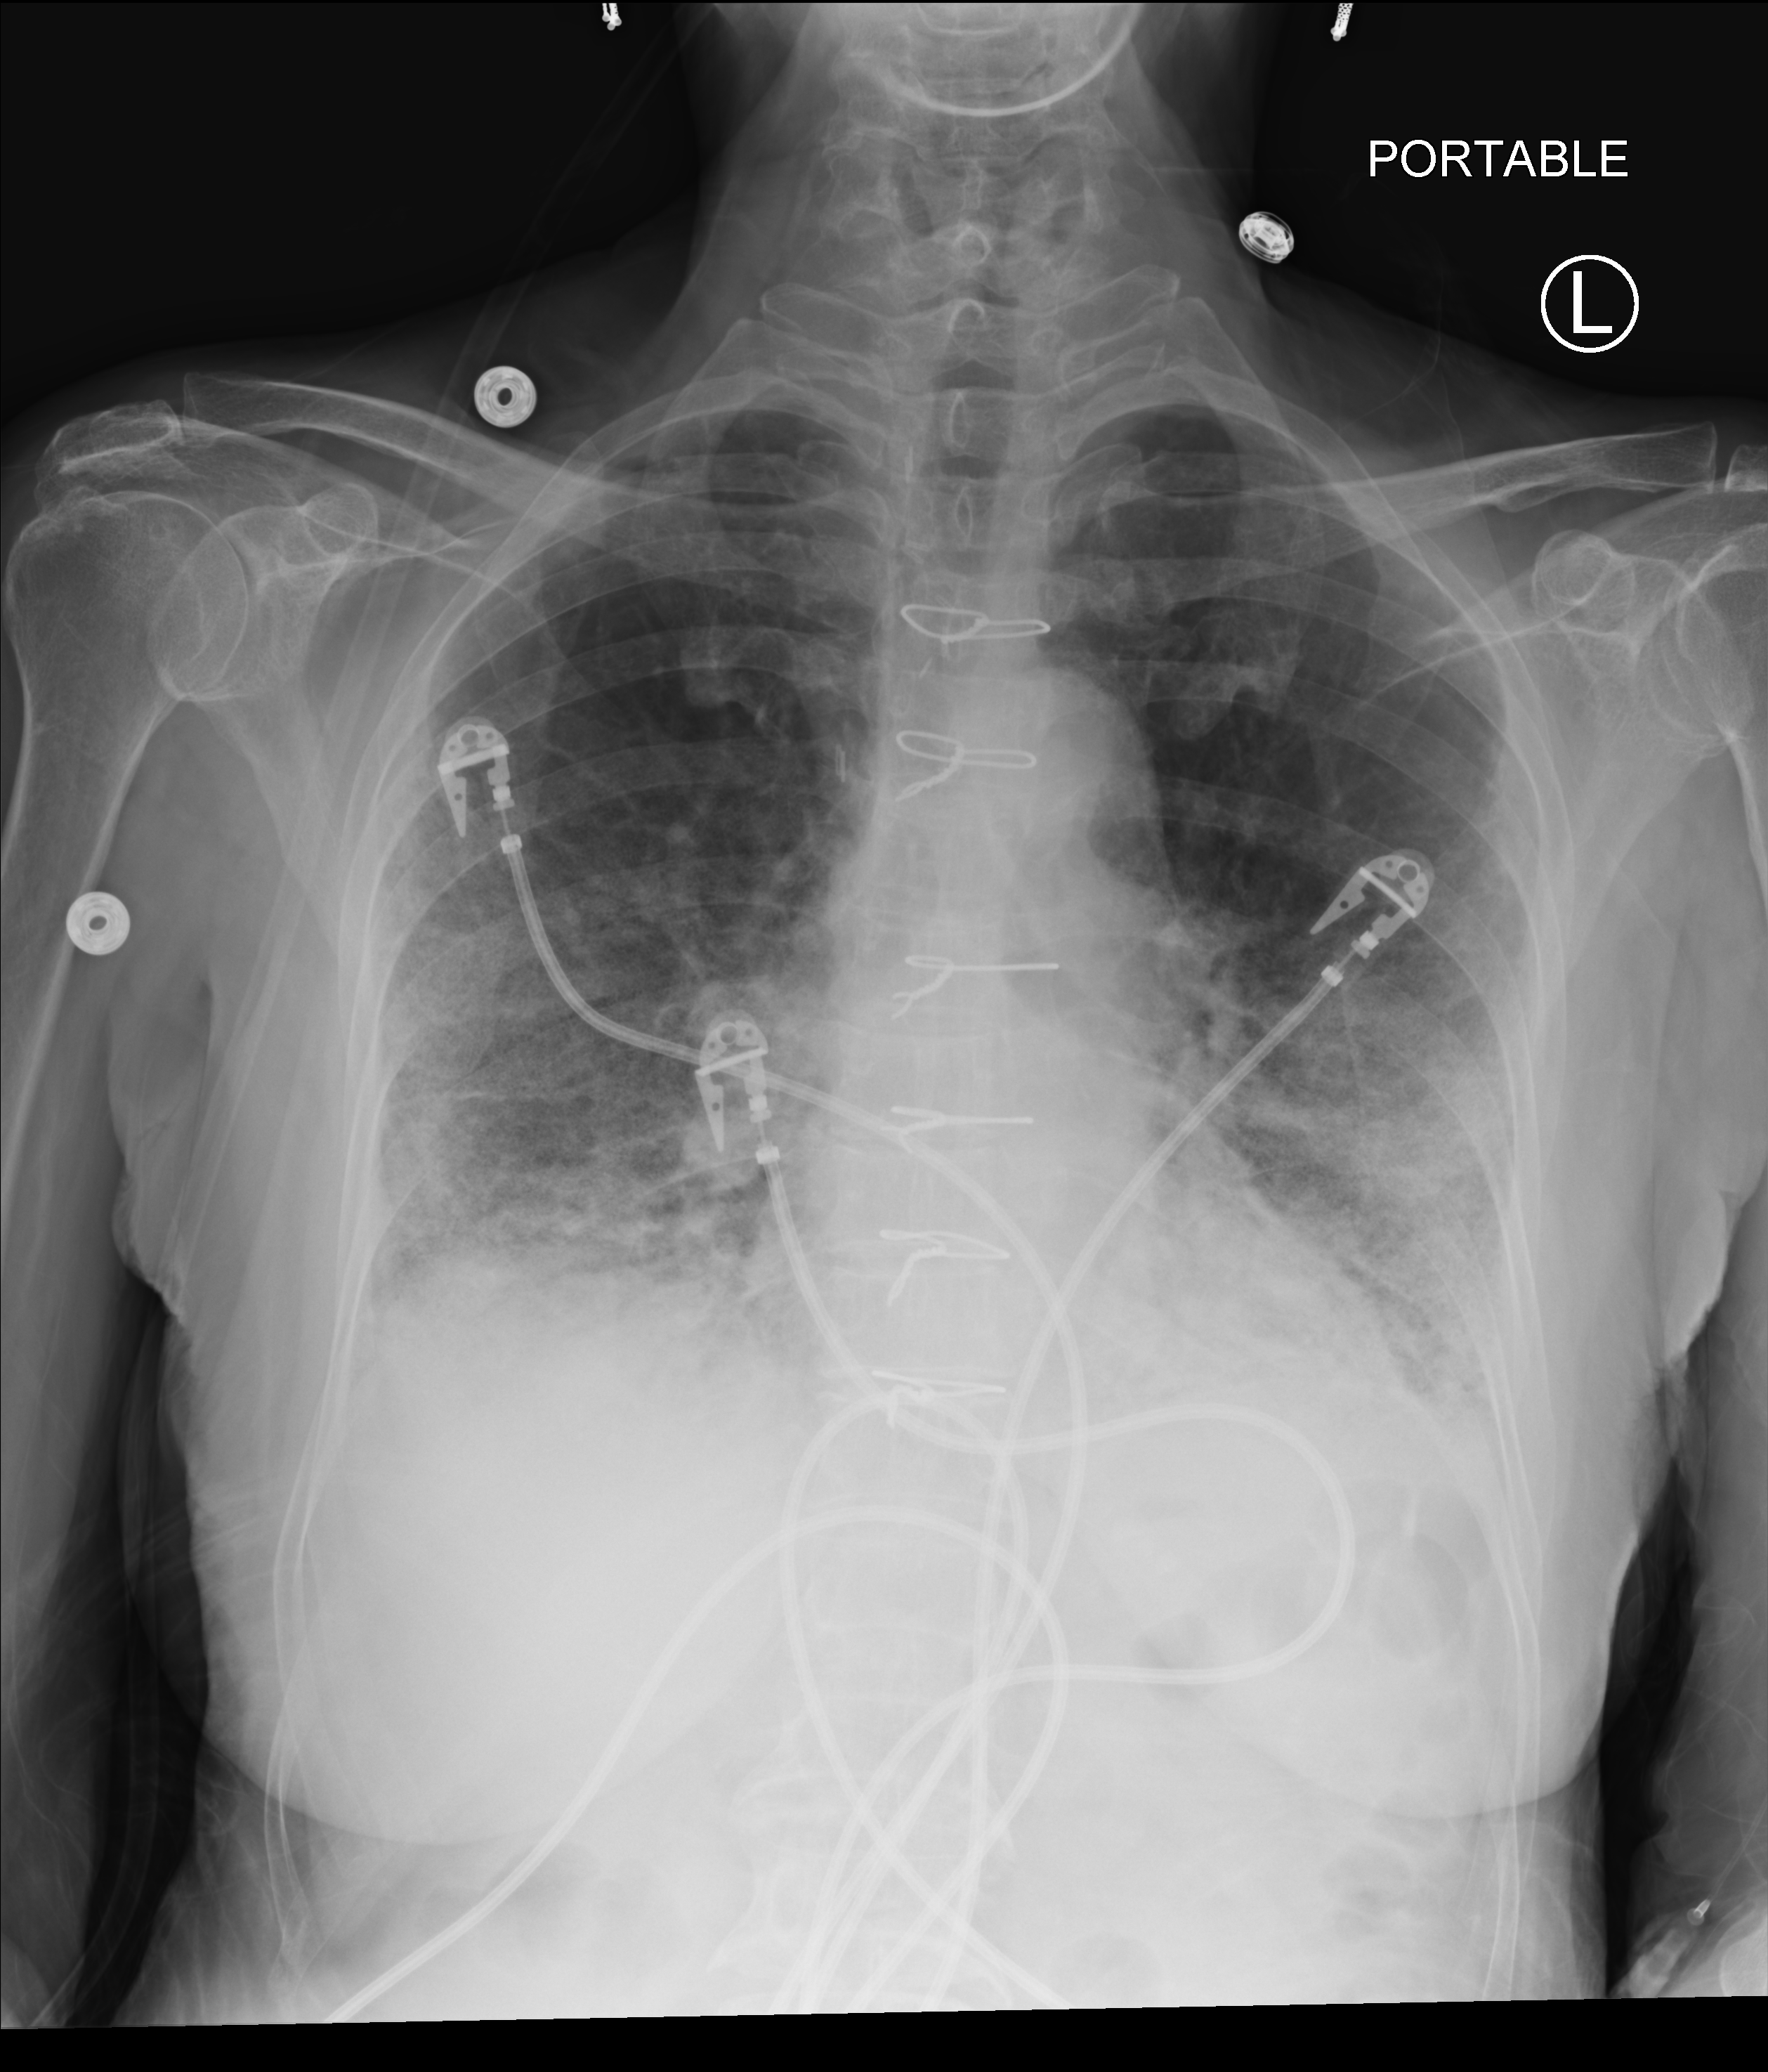
Bedside chest radiograph (computed radiography), anteroposterior (AP) projection. Female patient hospitalised with COVID-19, age 75–90 years.
Admission-level facts for this patient (not findings on this image; timing relative to this image not recorded):
- admitted to intensive care during this hospital stay: no
- smoking status (admission record): never